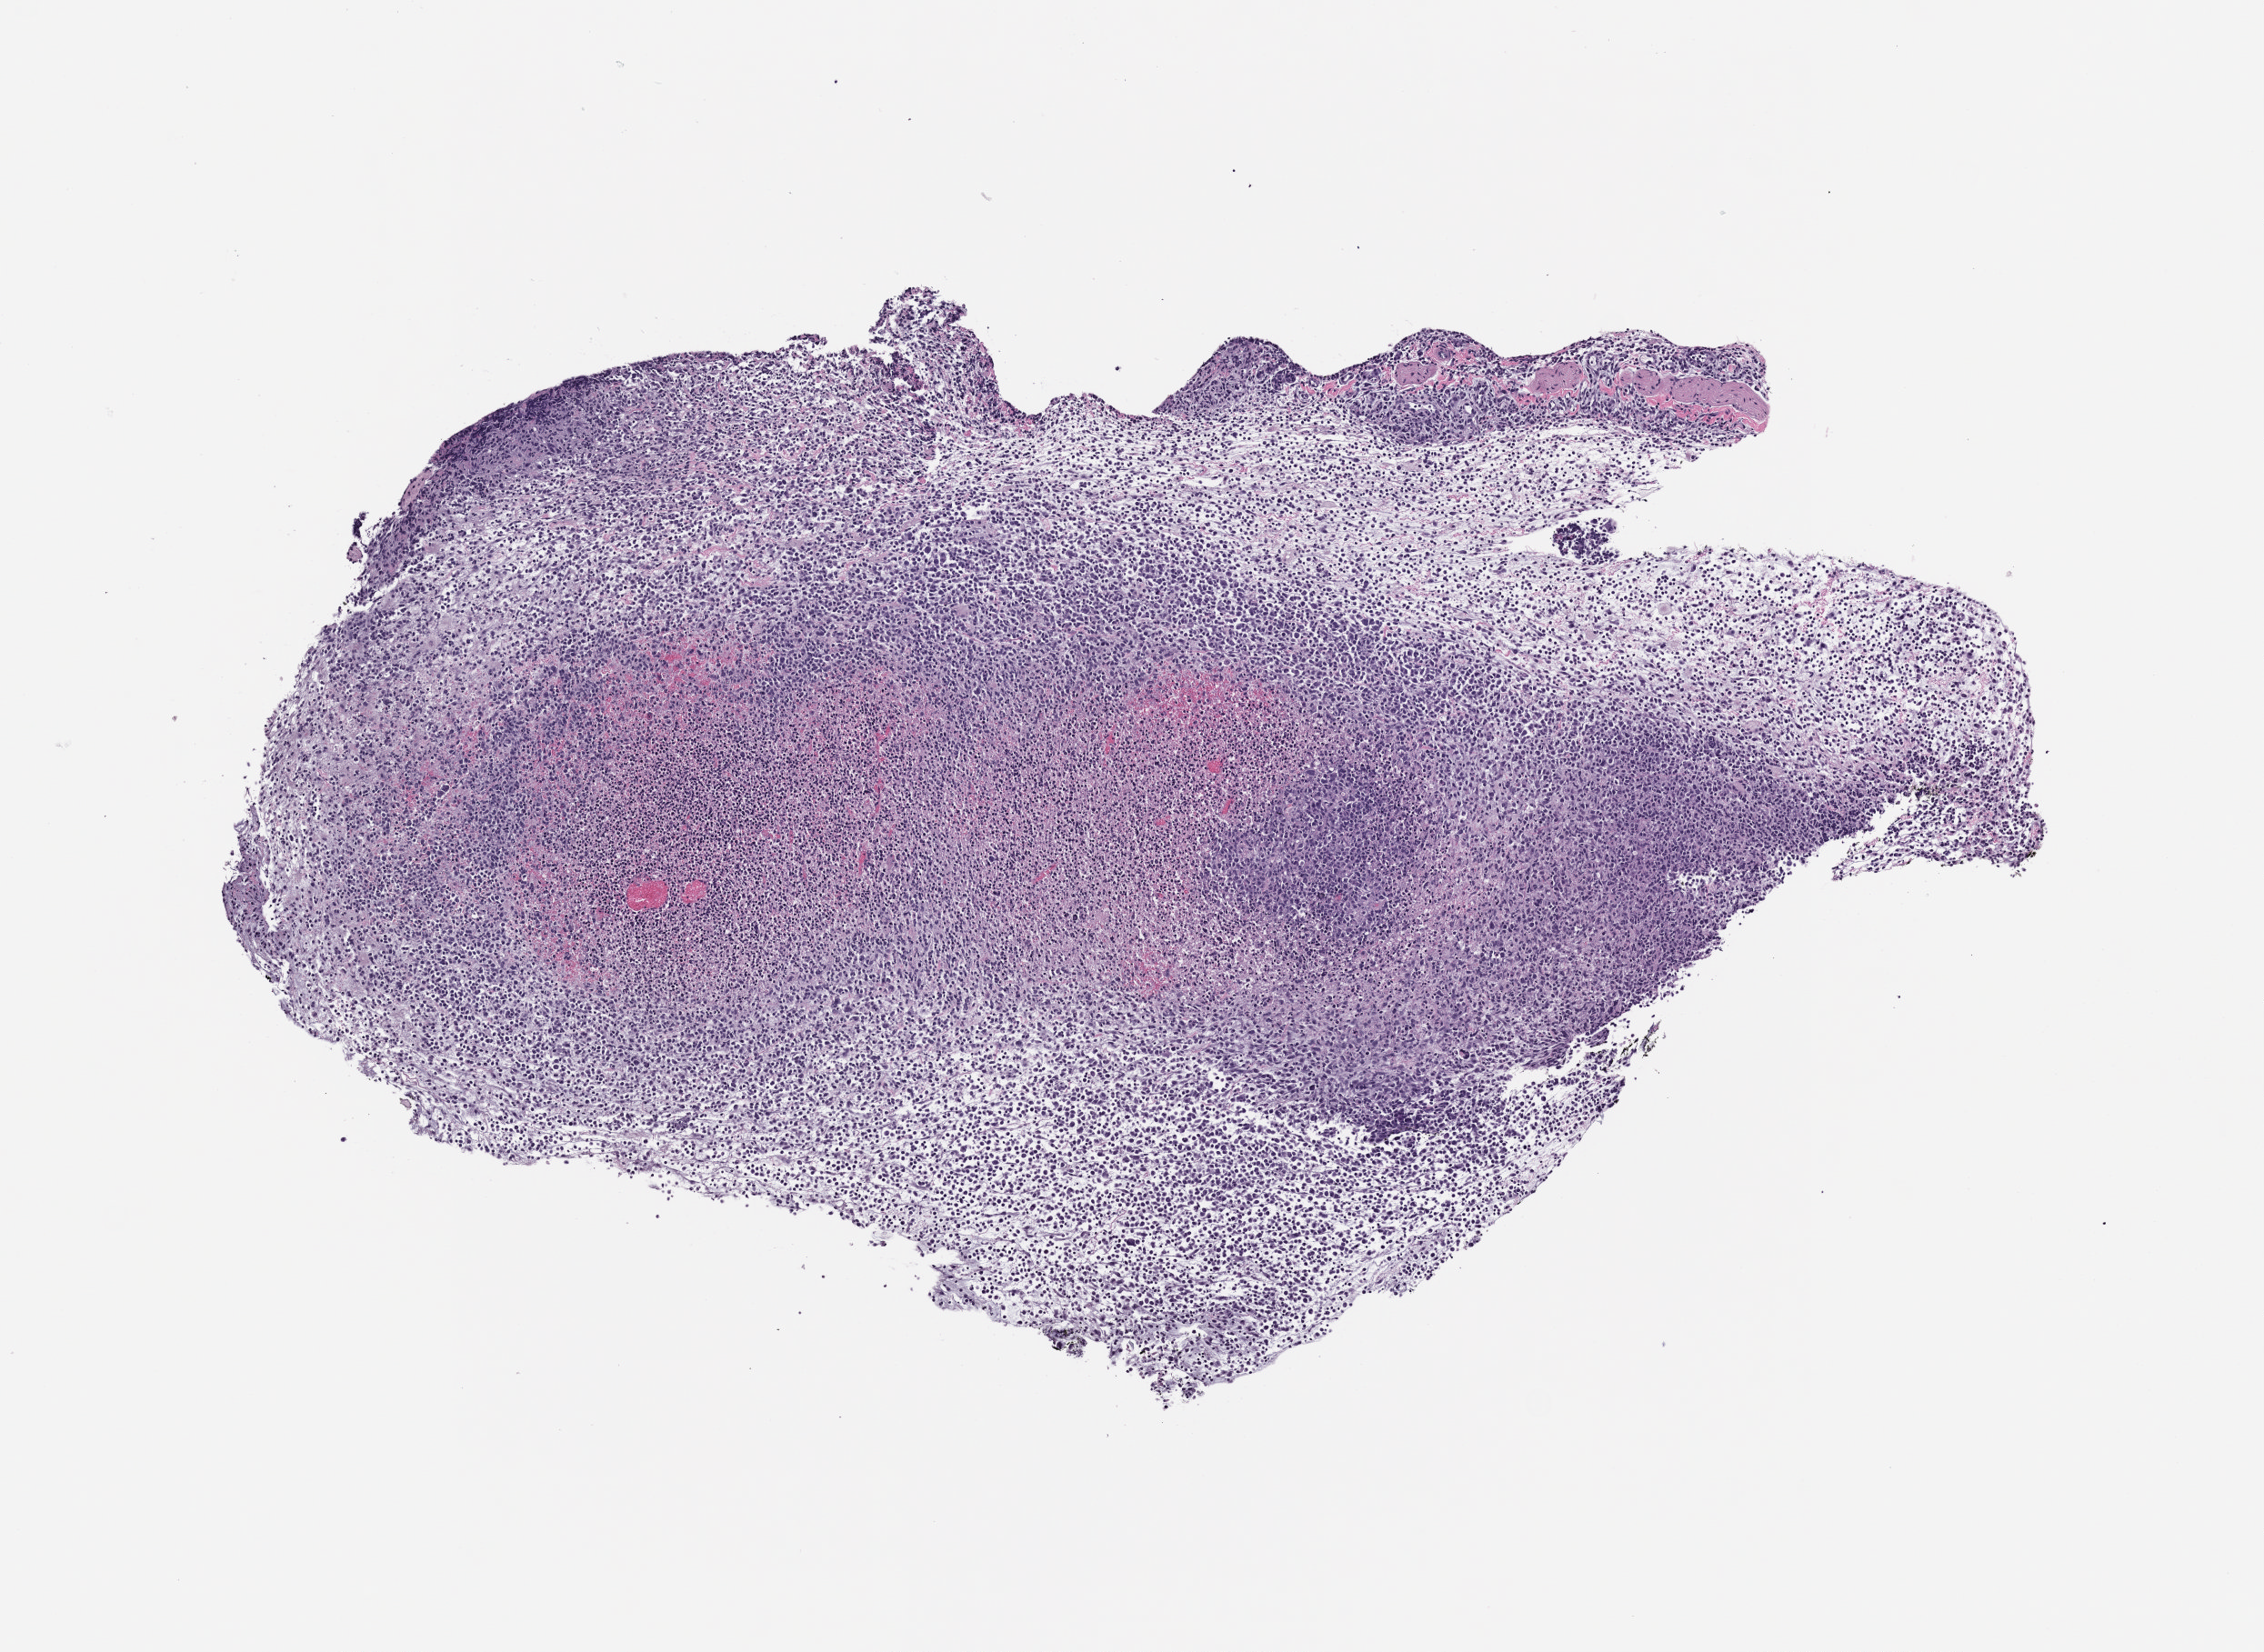
H&E whole-slide image of a patient-derived xenograft (PDX) tumor grown in a mouse — a low-resolution overview of the entire scanned area, about 5.0 x 3.7 mm.
Specimen: FFPE section.